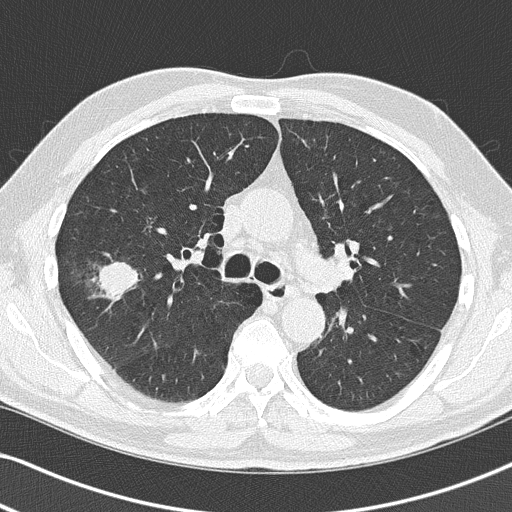
Low-dose screening chest CT, one axial slice; position 84 of 140 along the scan axis; 120 kVp; lung window (W 1500 / L -600 HU); 2 mm slice thickness; 512 × 512 image matrix, field of view 330 × 330 mm.
Structures marked on this image (expert manual segmentation):
- lesion 1 (tumor, upper lobe of right lung): bounding box (x1, y1, x2, y2) in pixels: (99, 262, 139, 295)